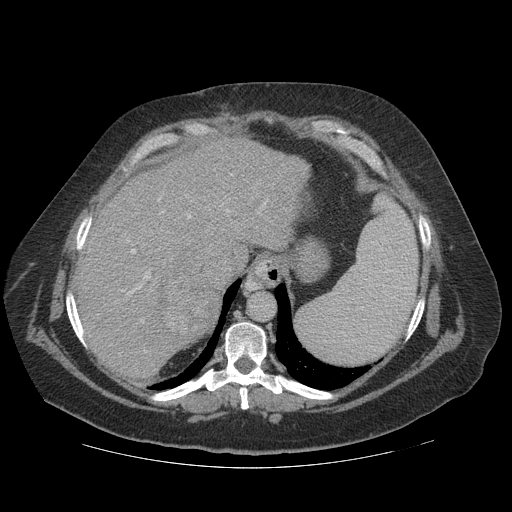
Contrast-enhanced abdominal CT (liver protocol), one axial slice; slice 91 of 121 in the series (ordered by position); reconstruction kernel STANDARD; 140 kVp; soft-tissue window (W 400 / L 40 HU); 2.5 mm slice thickness; 512 × 512 image matrix, field of view 420 × 420 mm. Case-level facts recorded for this patient, not image findings: diagnosis: hepatocellular carcinoma (patient treated with transarterial chemoembolisation; whether this scan precedes or follows treatment is not stated here); TNM stage (as recorded): Stage-IIIA; Child-Pugh class: A; tumour nodularity: multinodular; tumour size: 7.4 cm.
Outlined on this slice (semi-automatically segmented with operator editing):
- abdominal aorta: box from (x=249, y=292) to (x=274, y=321) px
- liver parenchyma outside the tumour (the mass and vessels are separate outlines, so this box may not span the whole liver): (x=72, y=138)–(x=310, y=379)
- mass: (x=157, y=264)–(x=219, y=350)
- liver vessels: (x=120, y=173)–(x=267, y=353)